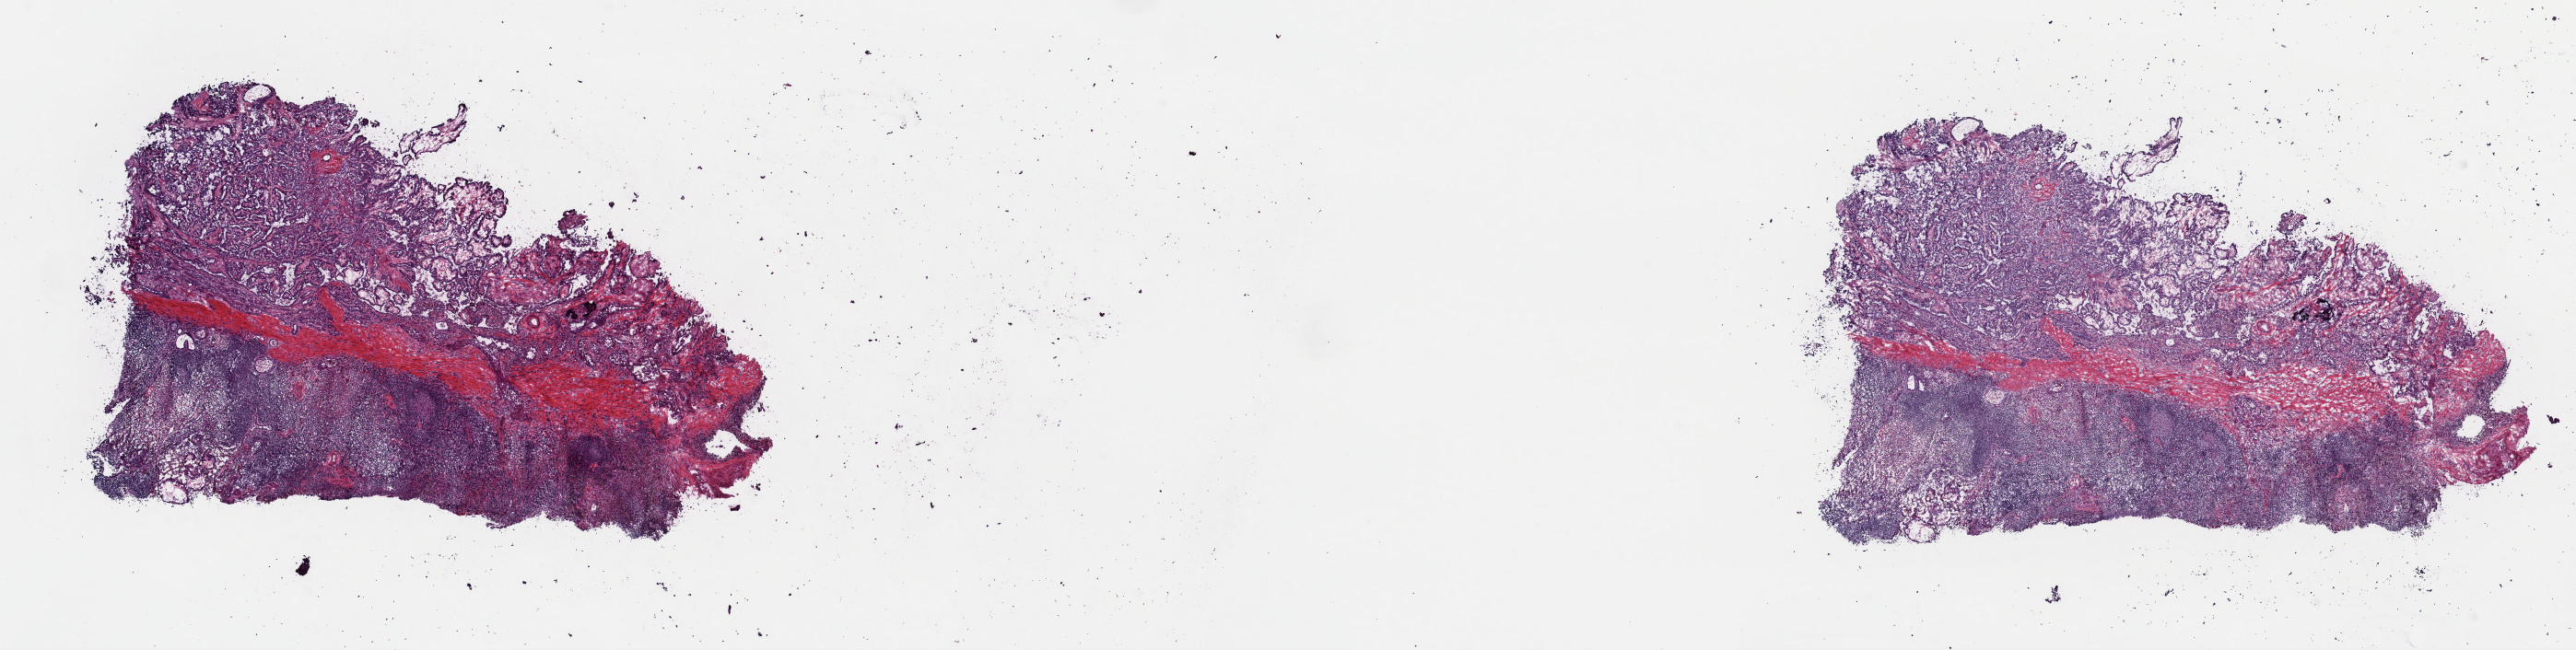
H&E whole-slide image — low-resolution overview of the scanned area, about 22.1 x 5.6 mm (acquisition: 40x scan), frozen section from the top of the tissue portion, metastatic tumour sample. Female patient; age at initial diagnosis 43 years.
This section: metastatic tumour tissue. Patient diagnosis: Papillary adenocarcinoma, NOS.